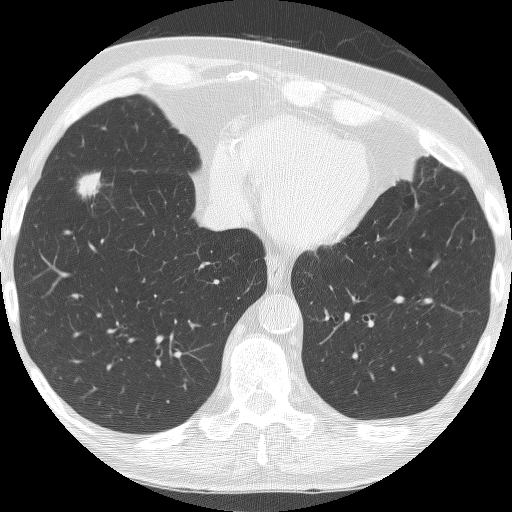
Axial slice from a low-dose chest CT screening exam, baseline screening round, lung window (W 1500 / L -600 HU), lung (sharp) reconstruction kernel (BONE), 120 kVp, slice 118 of 182 in the series. Male, age 74 years at enrolment. Former smoker at enrolment.
- Expert-annotated lung lesion, box from (x=68, y=165) to (x=119, y=206) px.
- The screening reader recorded 4 non-calcified nodules or masses ≥4 mm on this exam; which of them this box marks is not recorded.
- Participant outcome: lung cancer diagnosed 35 days after this screen — bronchiolo-alveolar carcinoma, mucinous, right lower lobe, well differentiated (G1), stage IA (AJCC 6th edition), 22 mm at pathology.